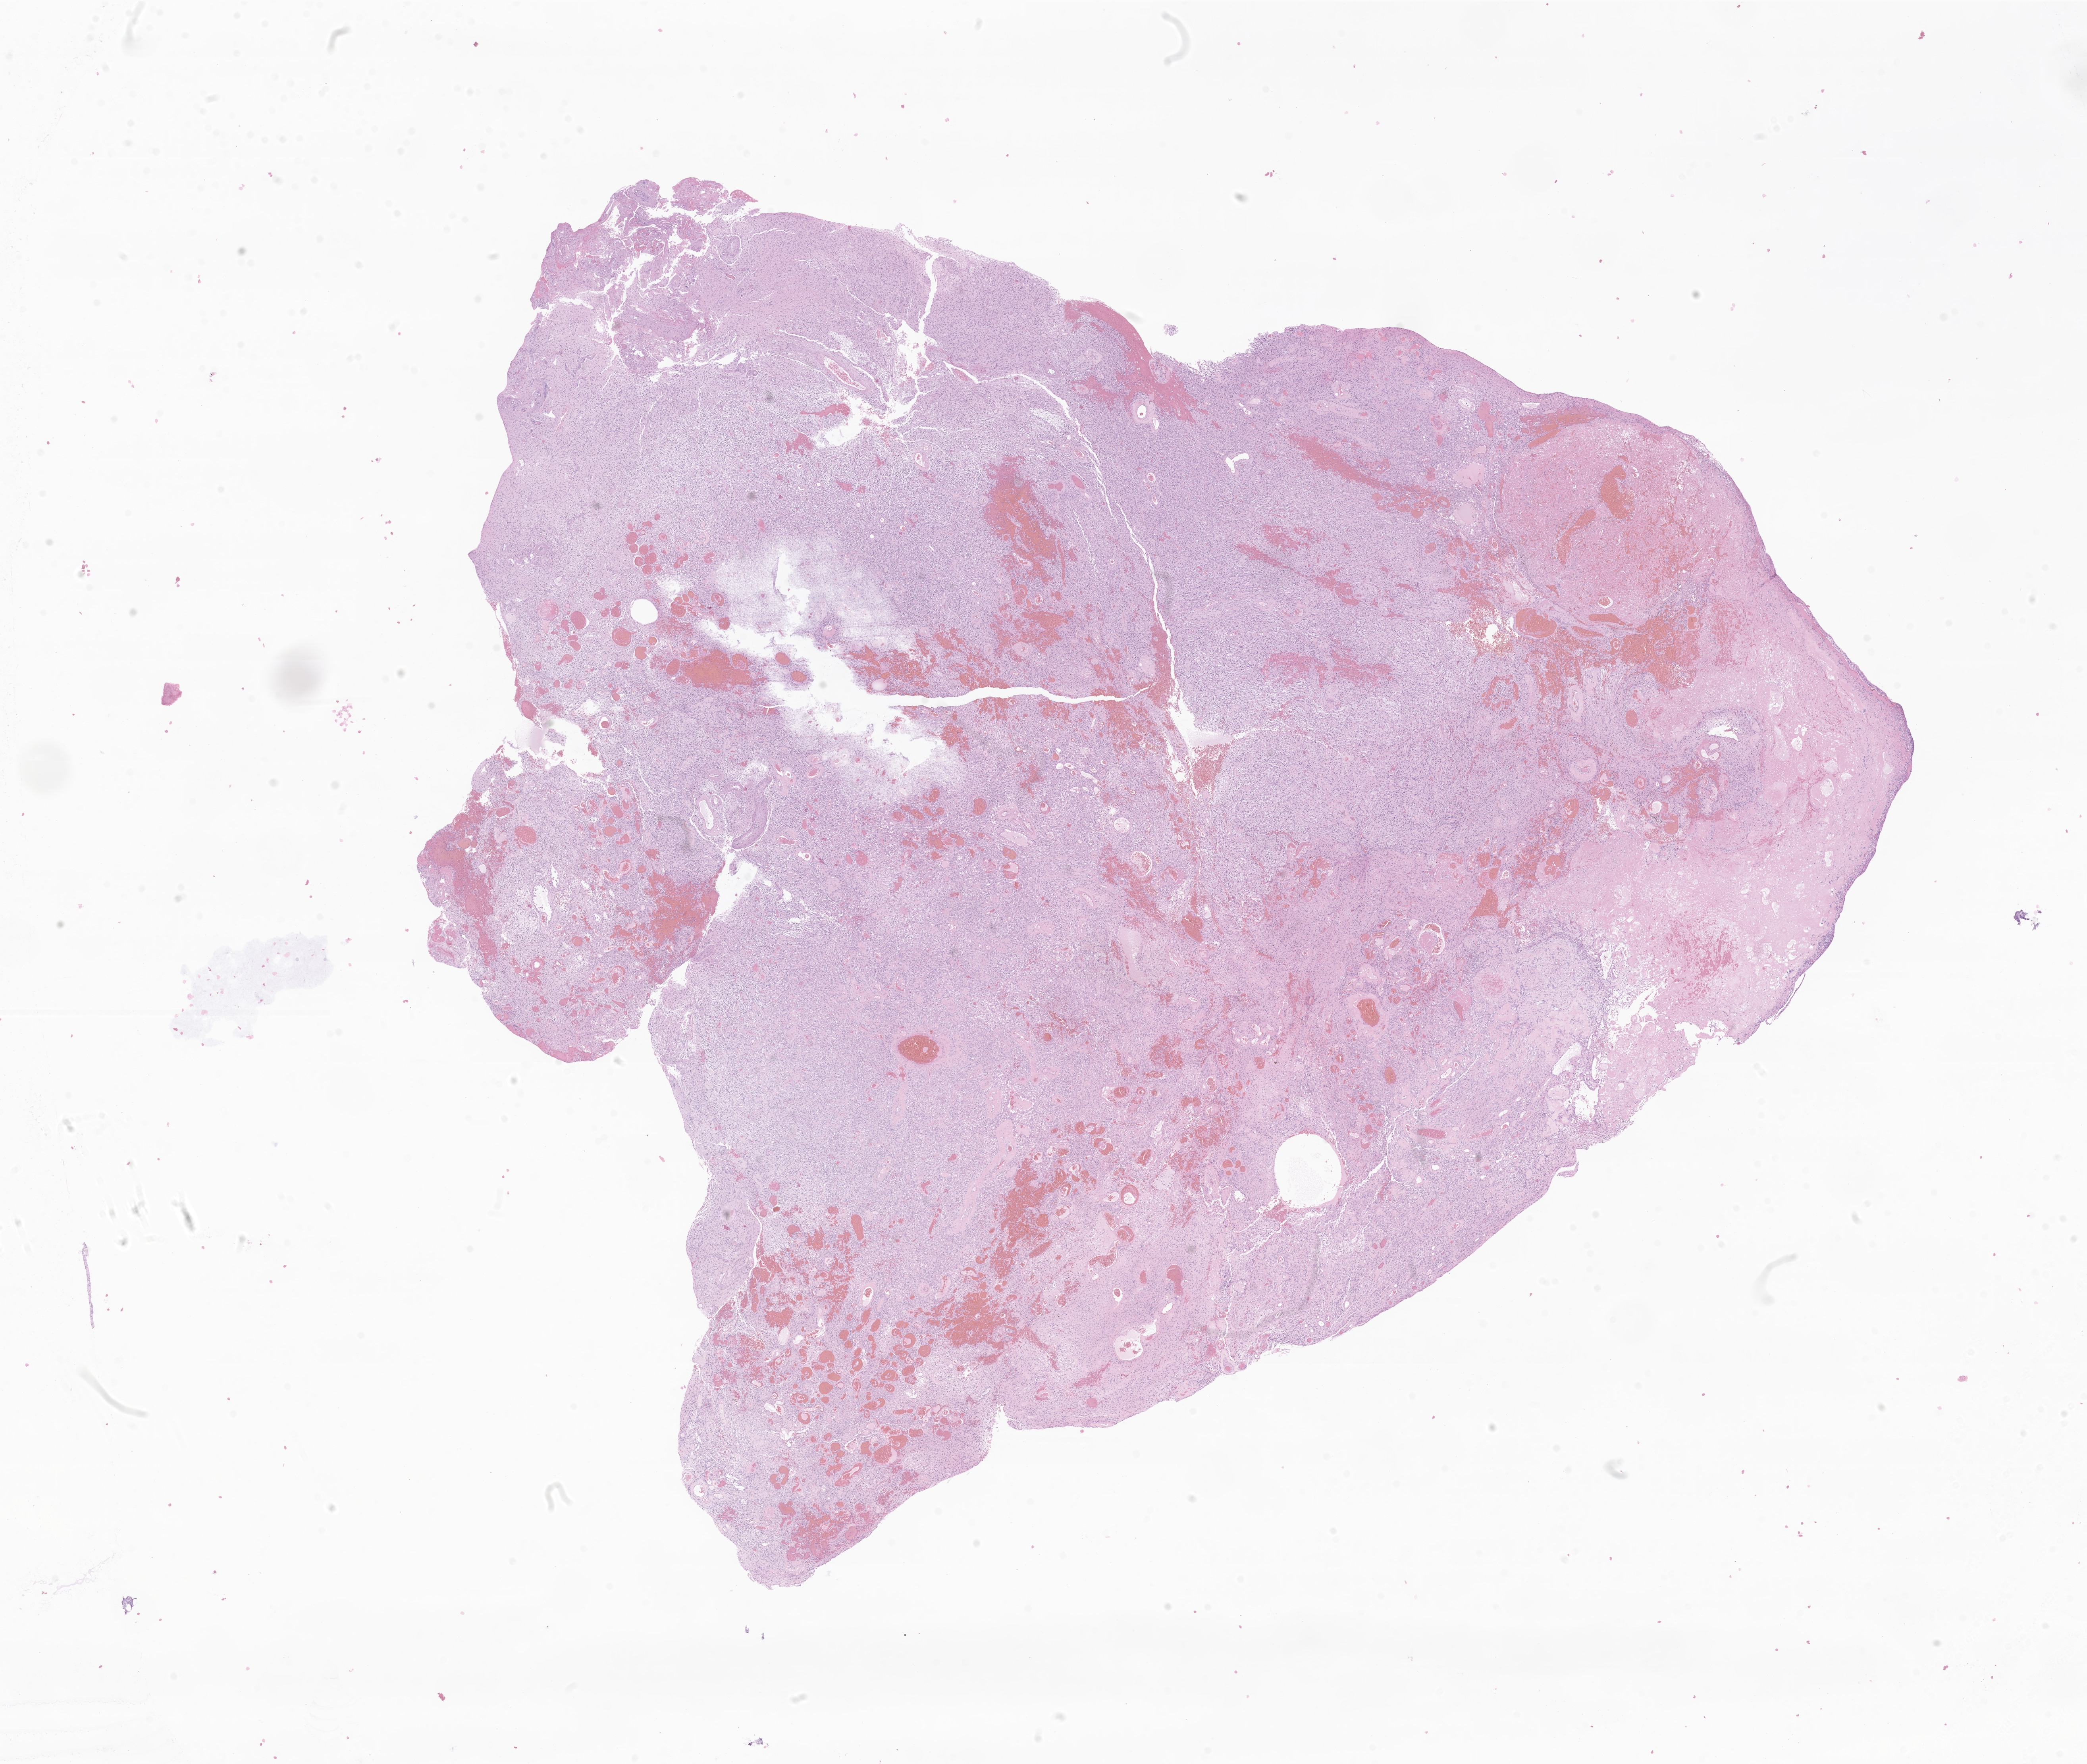
Whole-slide image, H&E stain of tumor tissue from the brain — whole scanned area (about 22.2 x 18.7 mm) shown as a low-resolution overview; formalin-fixed, paraffin-embedded (FFPE) tissue. Female patient, age 144 months (12 years).
- diagnosis: Pilocytic astrocytoma